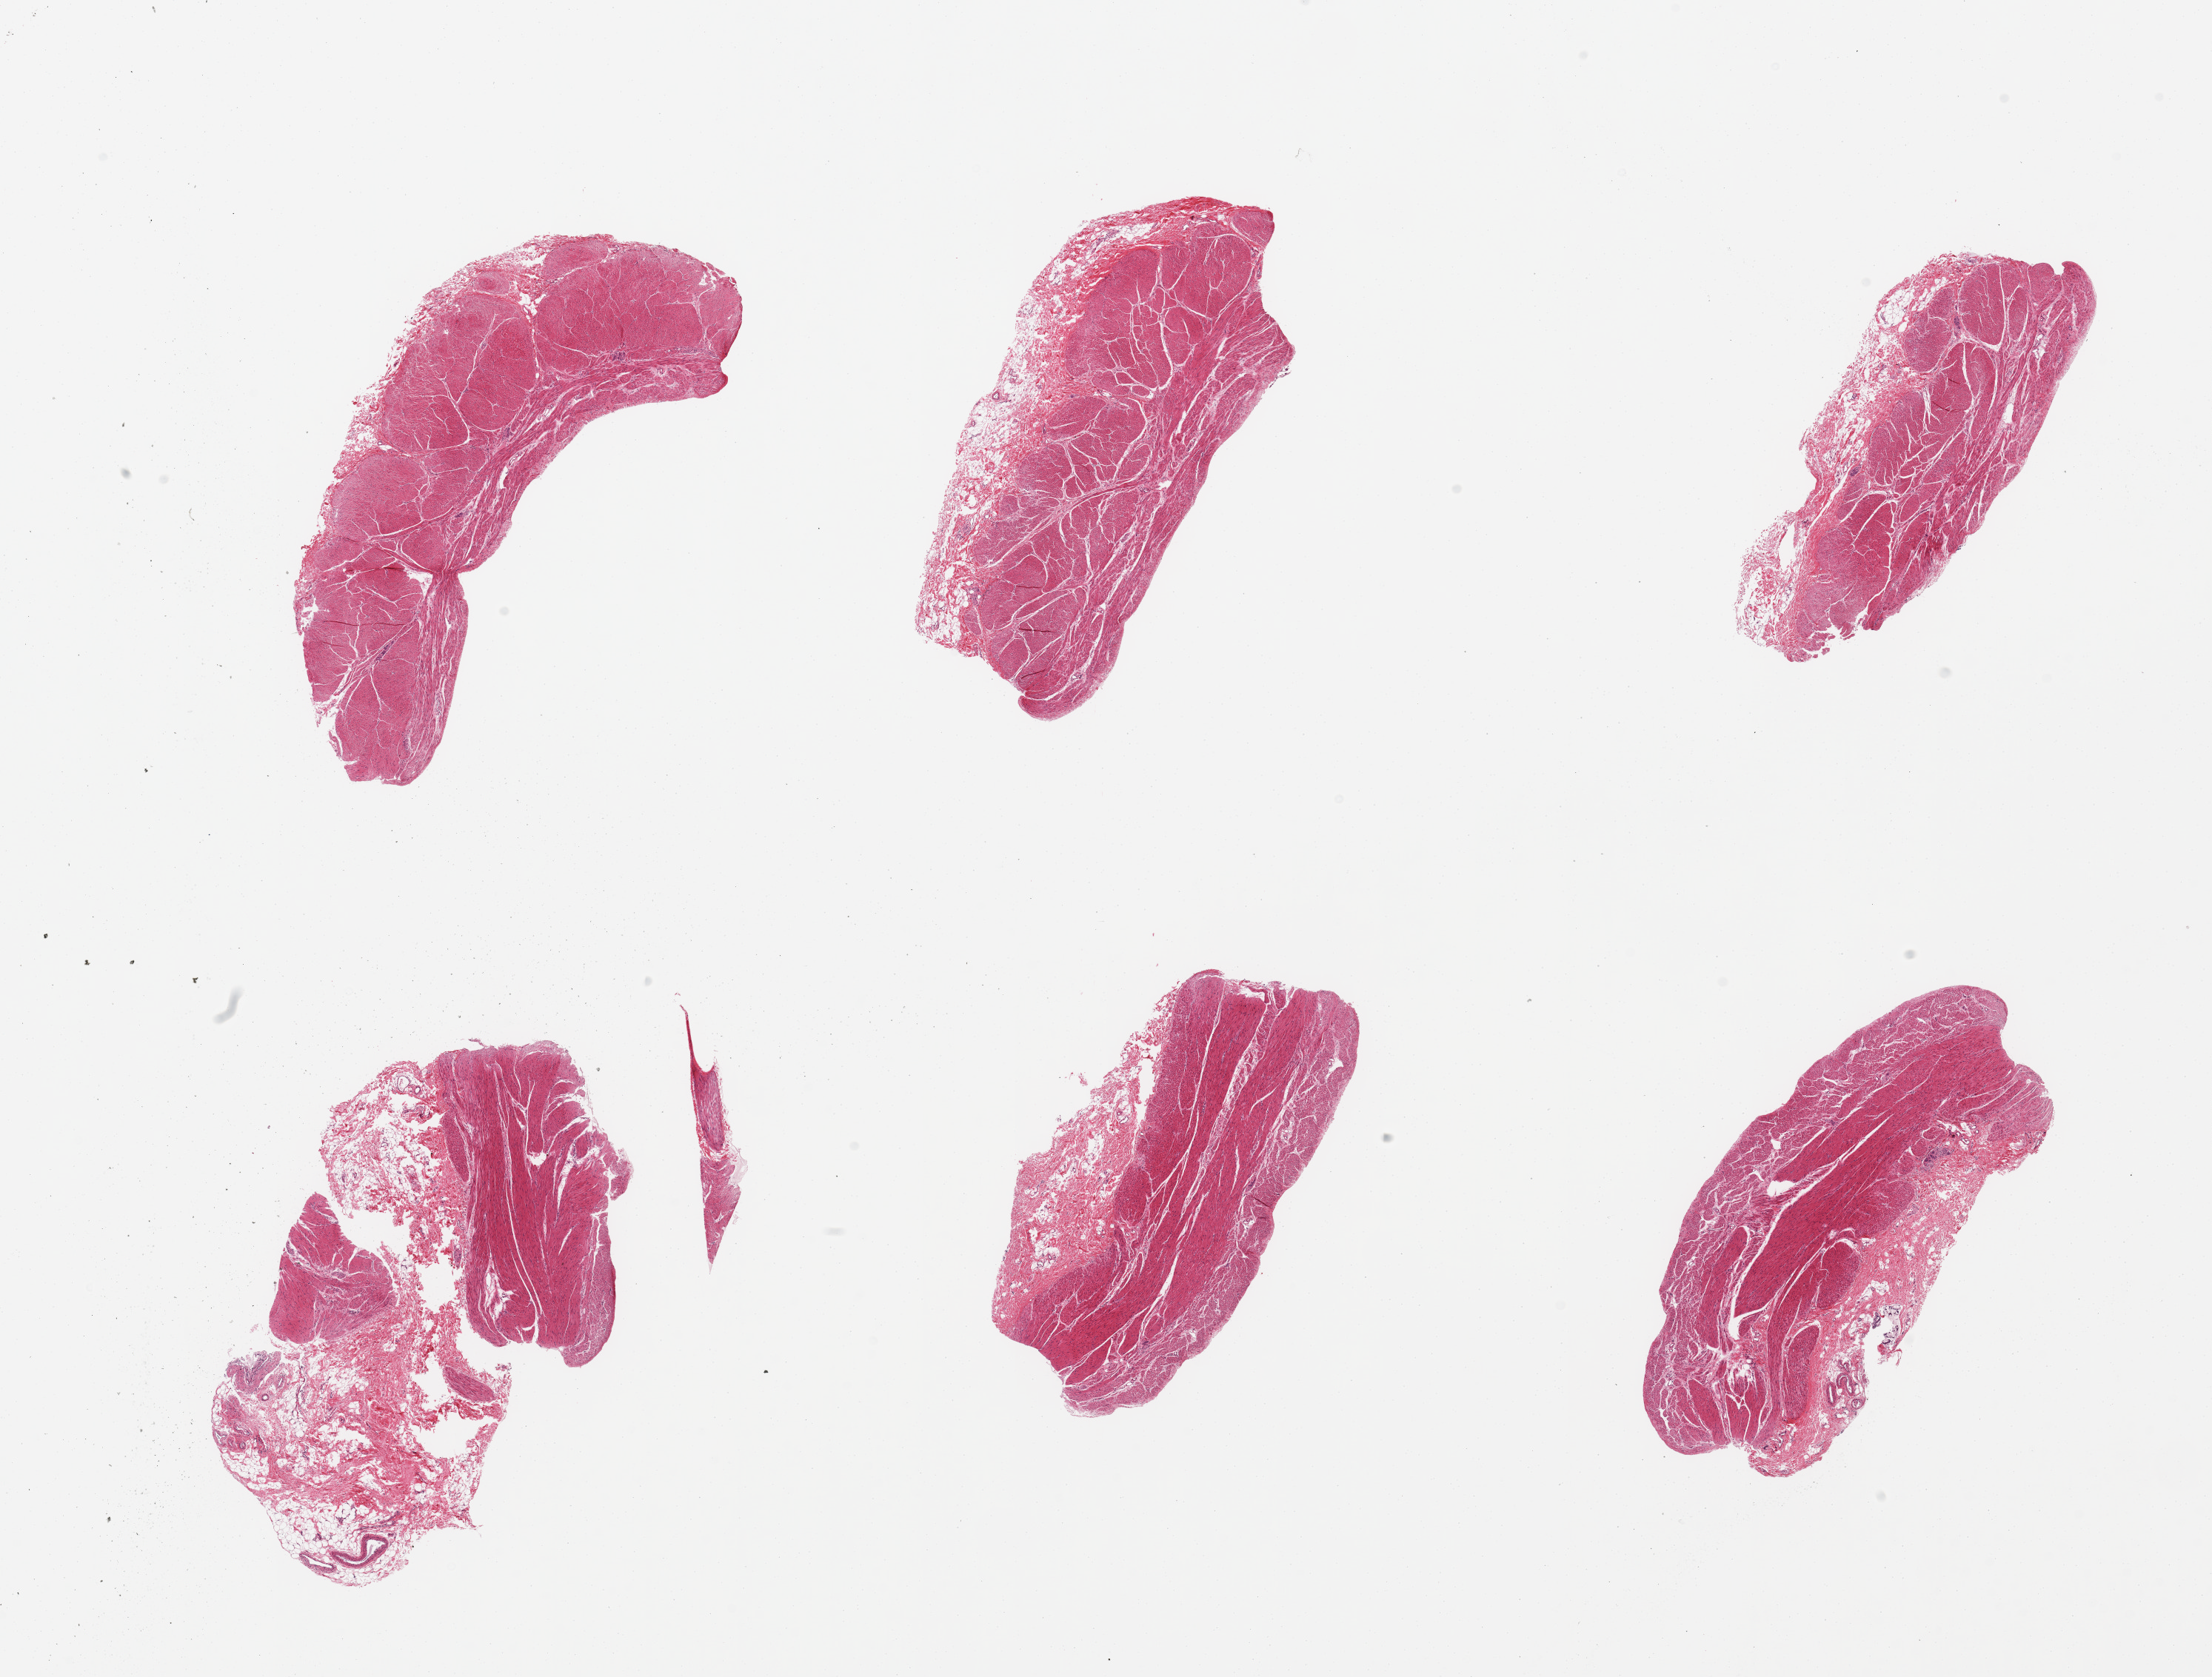
H&E whole-slide image — shown as a low-resolution overview of the whole scanned area (about 23.6 x 17.9 mm), PAXgene-fixed paraffin-embedded (PFPE) section, target tissue: stomach, donor tissue sample.
- reviewer comment on this tissue sample: 6 pieces; no mucosa, only muscularis propria and submucosa